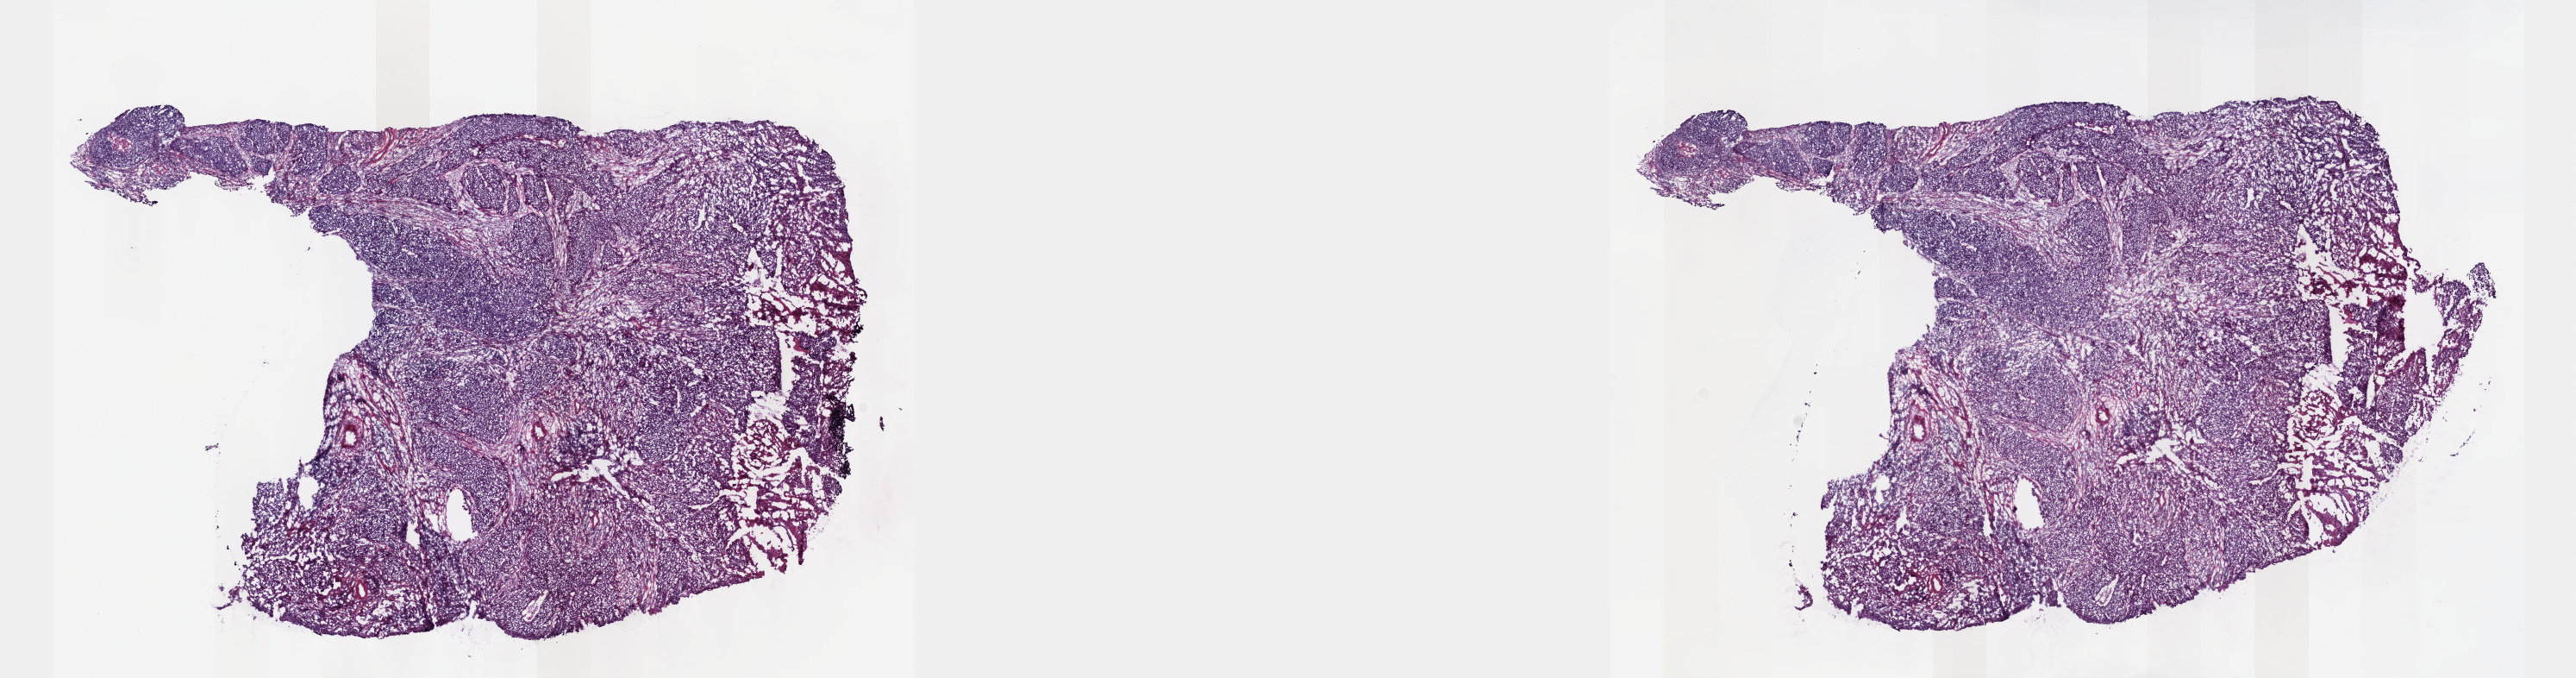
Whole-slide histology image, H&E-stained, a low-resolution overview of the entire scanned area, about 24.1 x 6.4 mm (acquisition: 40x scan). Frozen section from the top of the tissue portion. Primary tumour sample from the cervix. Patient: female, age at initial diagnosis 33 years. Histologic grade: G2 (moderately differentiated). Composition of this section per pathologist review: tumour cells 75%, tumour nuclei 75%, normal cells 5%, stromal cells 20%, necrosis 0%. Inflammatory infiltration, as recorded: lymphocyte infiltration 5%, monocyte infiltration 0%, neutrophil infiltration 0%.
• histologic diagnosis: Squamous cell carcinoma, NOS (cervix uteri)
• FIGO stage: IIB